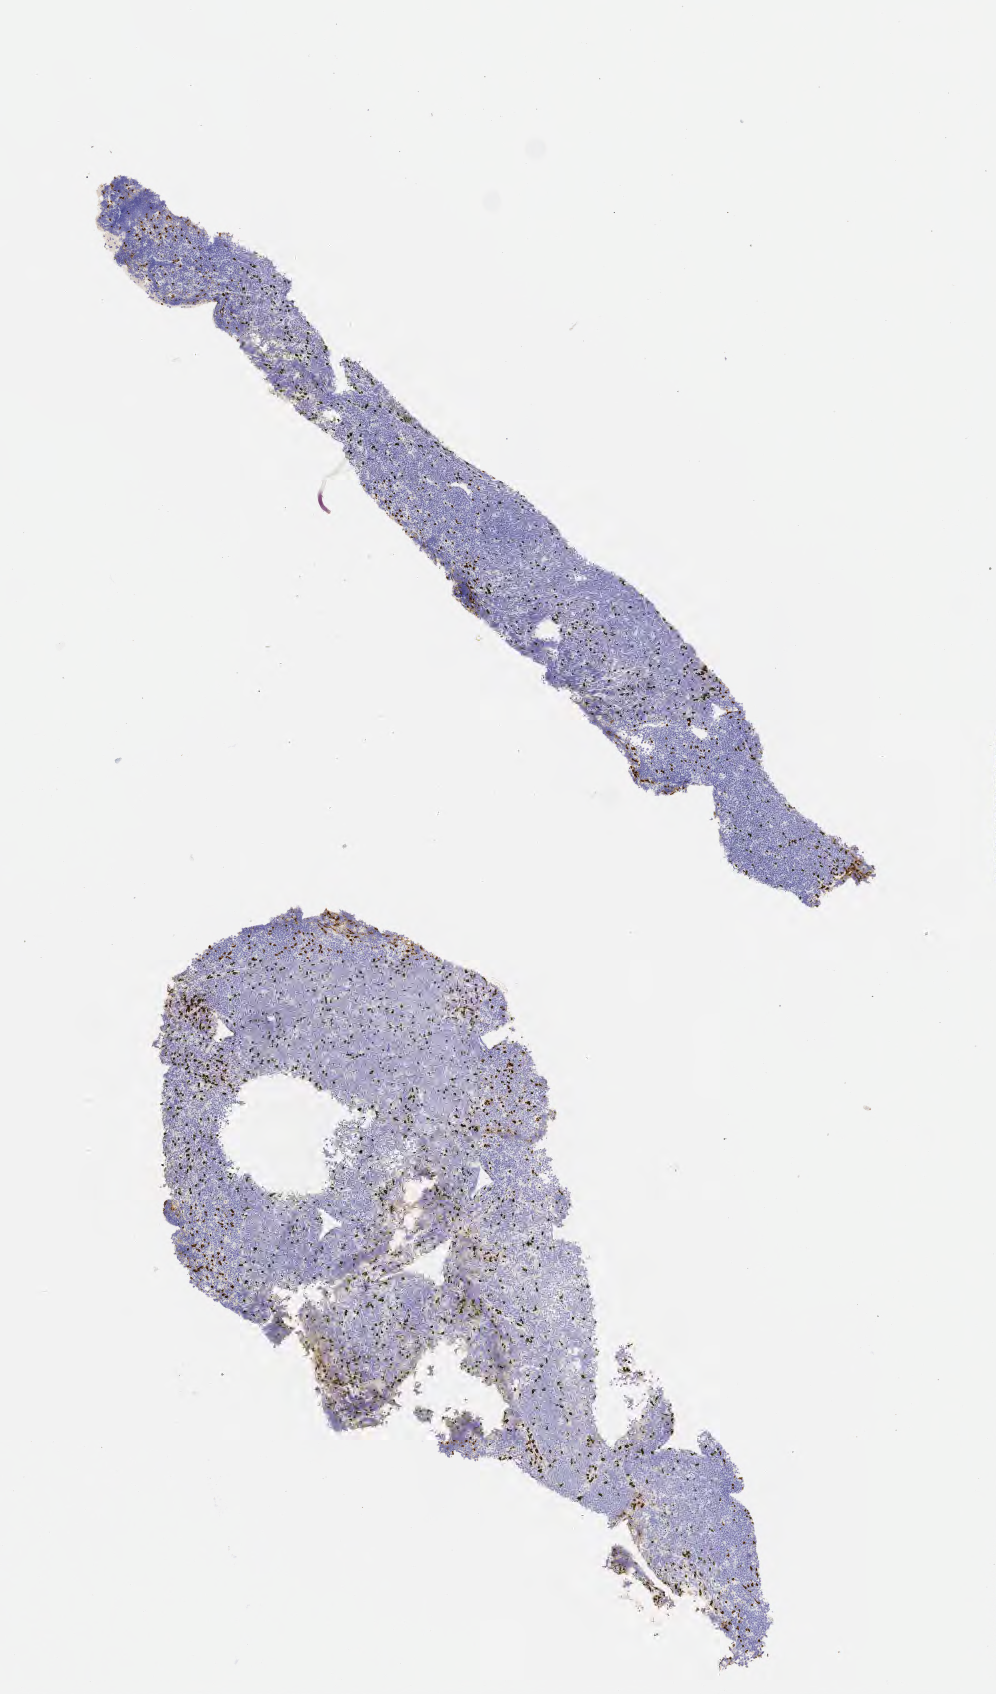
IHC for CD3, whole-slide image — whole scanned area (about 4.0 x 6.8 mm) shown as a low-resolution overview, tumor tissue. Male, age 8 years at initial diagnosis.
Diagnosis: Burkitt lymphoma, NOS.